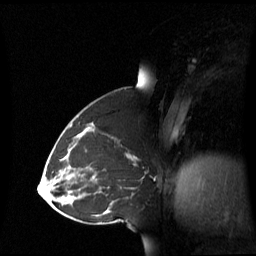
Breast MRI (dynamic contrast-enhanced), one sagittal slice. Position 33 of 60 along the scan axis. Dynamic contrast-enhanced series, image 2 of 3 at this slice position (ordered by acquisition). 1.5 T. TE 4.2 ms, TR 8.4 ms. 2.8 mm slice thickness. 256 × 256 image matrix, field of view 270 × 270 mm. Female patient, age 43 years. From the clinical record (not read from this slice): setting: breast cancer imaged before/during neoadjuvant chemotherapy; receptor status: triple-negative.
Structures marked on this image (semi-automatically segmented with operator editing):
- analysis volume of interest (the breast-tissue region the enhancement analysis was run in; not a lesion): bounding box (x1, y1, x2, y2) in pixels: (69, 137, 143, 198)
- tumour enhancement mask (voxels above the 70 % enhancement threshold inside the analysis volume of interest): (74, 137, 137, 159)